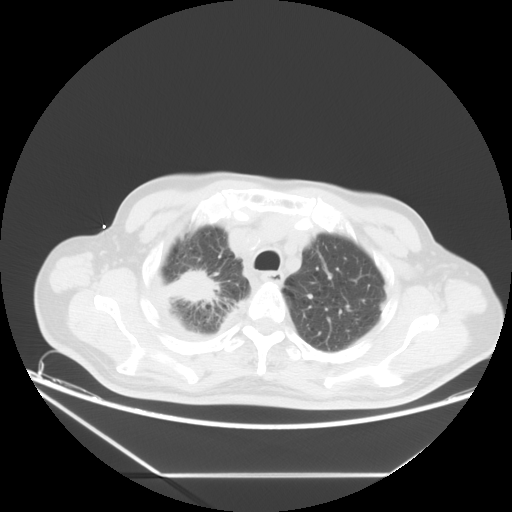
Chest CT, one axial slice. Slice 15 of 20 in the series (ordered by position). Reconstruction kernel STANDARD. Lung window (W 1500 / L -600 HU). 512 × 512 image matrix, field of view 418 × 418 mm. Patient: male, 75 years. Case-level facts recorded for this patient, not image findings: clinical TNM (as recorded): T1c N1 M1.
Structures marked on this image (bounding box drawn by a radiologist):
- lung tumour (recorded histology: adenocarcinoma): bounding box [x1, y1, x2, y2] px = [161, 267, 222, 306]